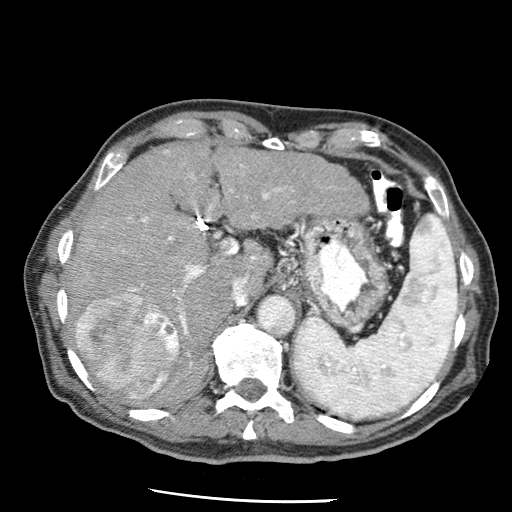
Contrast-enhanced abdominal CT (liver protocol), one axial slice; slice 41 of 79 in the series (ordered by position); reconstruction kernel STANDARD; soft-tissue window (W 400 / L 40 HU); 2.5 mm slice thickness; 512 × 512 image matrix, field of view 320 × 320 mm. Case-level facts recorded for this patient, not image findings: diagnosis: hepatocellular carcinoma (patient treated with transarterial chemoembolisation; whether this scan precedes or follows treatment is not stated here); TNM stage (as recorded): Stage-IIIA; Child-Pugh class: A; tumour differentiation: moderately differentiated; tumour nodularity: multinodular.
Outlined on this slice (semi-automatic segmentation, software-assisted and operator-edited):
- liver parenchyma outside the tumour (the mass and vessels are separate outlines, so this box may not span the whole liver): box from (x=64, y=144) to (x=368, y=404) px
- mass: (x=75, y=287)–(x=179, y=399)
- liver vessels: (x=129, y=150)–(x=283, y=366)